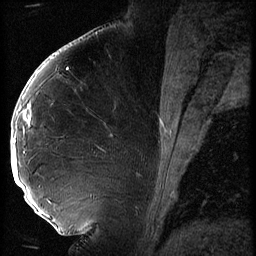
Breast MRI (dynamic contrast-enhanced), one sagittal slice; 3 images stored at this slice position (order not interpretable as contrast timing); 1.5 T; TE 4.2 ms, TR 9 ms; 2.5 mm slice thickness; 256 × 256 image matrix, field of view 180 × 180 mm. Female patient, age 43 years. From the clinical record (not read from this slice): setting: breast cancer imaged before/during neoadjuvant chemotherapy; receptor status: HER2-positive.
Outlined on this slice (semi-automatic segmentation, software-assisted and operator-edited):
- analysis volume of interest (the breast-tissue region the enhancement analysis was run in; not a lesion): box from (x=11, y=92) to (x=74, y=211) px
- tumour enhancement mask (voxels above the 140 % enhancement threshold inside the analysis volume of interest): (x=12, y=106)–(x=31, y=181)